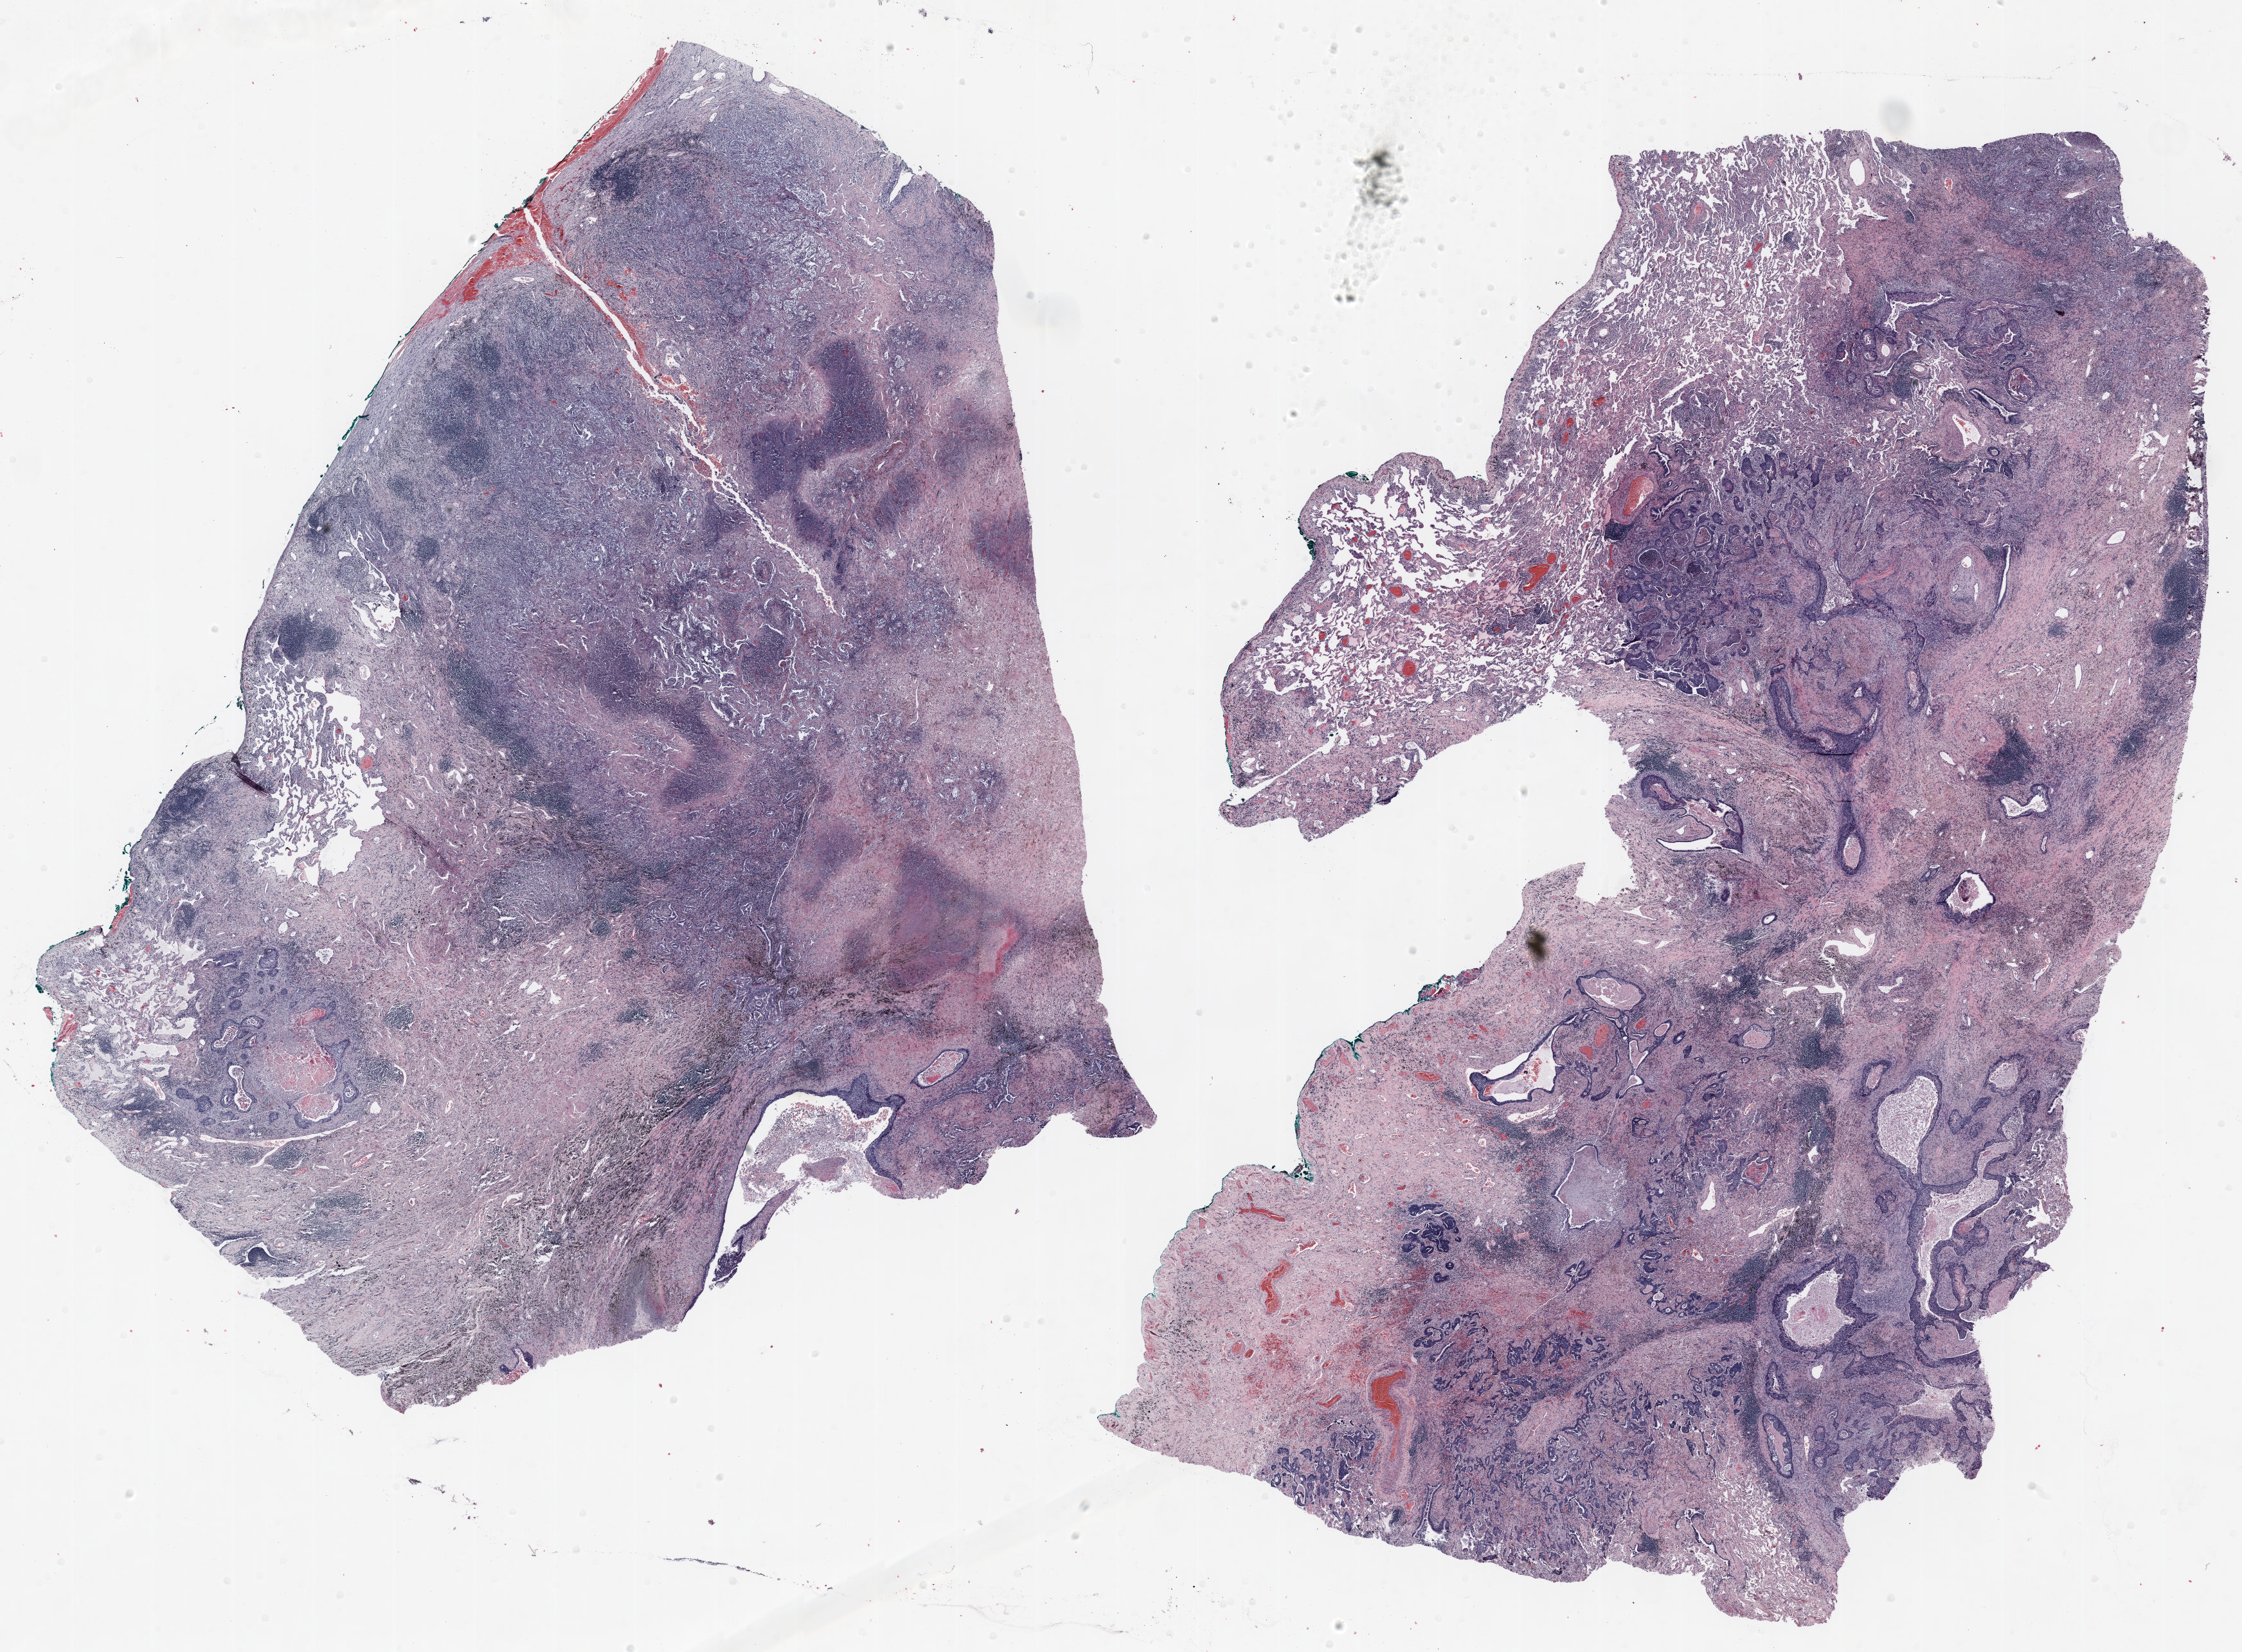
H&E whole-slide image — low-resolution overview of the scanned area, about 28.0 x 20.7 mm. Formalin-fixed paraffin-embedded (FFPE) section. Lung tissue. Male patient, aged 72 at enrolment. Former smoker at enrolment.
Participant's lung-cancer diagnosis: Adenosquamous carcinoma.